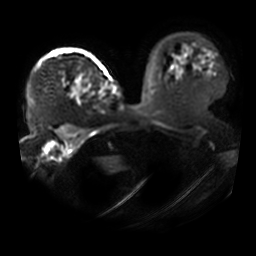
Breast MRI, one axial slice; position 32 of 41 along the scan axis; diffusion-weighted series; image 2 of 4 stored at this slice position (different b-values; order by instance number); 3 T; 256 × 256 image matrix. Female patient.
Outlined on this slice (outlined manually by an expert reader):
- tumour on diffusion-weighted imaging: box from (x=74, y=80) to (x=80, y=91) px